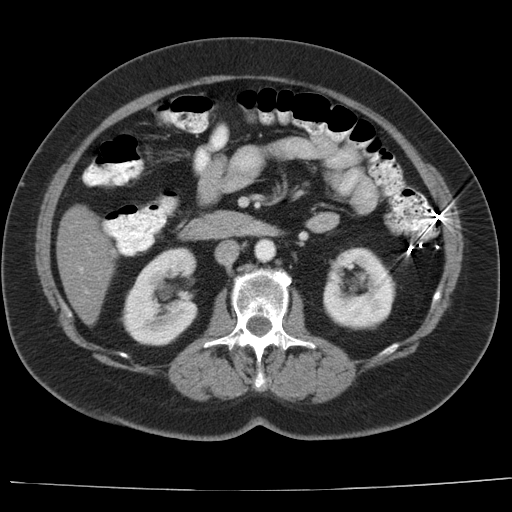
Contrast-enhanced abdominal CT, one axial slice; position 7 of 44 along the scan axis; reconstruction kernel AA-1; intravenous contrast given; soft-tissue window (W 400 / L 40 HU); 5 mm slice thickness; 512 × 512 image matrix, field of view 373 × 373 mm. Female patient. From the clinical record (not read from this slice): diagnosis: colorectal cancer liver metastases, imaged before liver resection; multiple liver metastases: yes; largest metastasis: 1.8 cm; chemotherapy before resection: yes.
Annotated regions visible in this slice (manually delineated by an expert):
- hepatic veins: box from (x=80, y=268) to (x=82, y=271) px
- liver: (x=58, y=207)–(x=117, y=324)
- portal vein (with intrahepatic branches): (x=85, y=291)–(x=88, y=293)